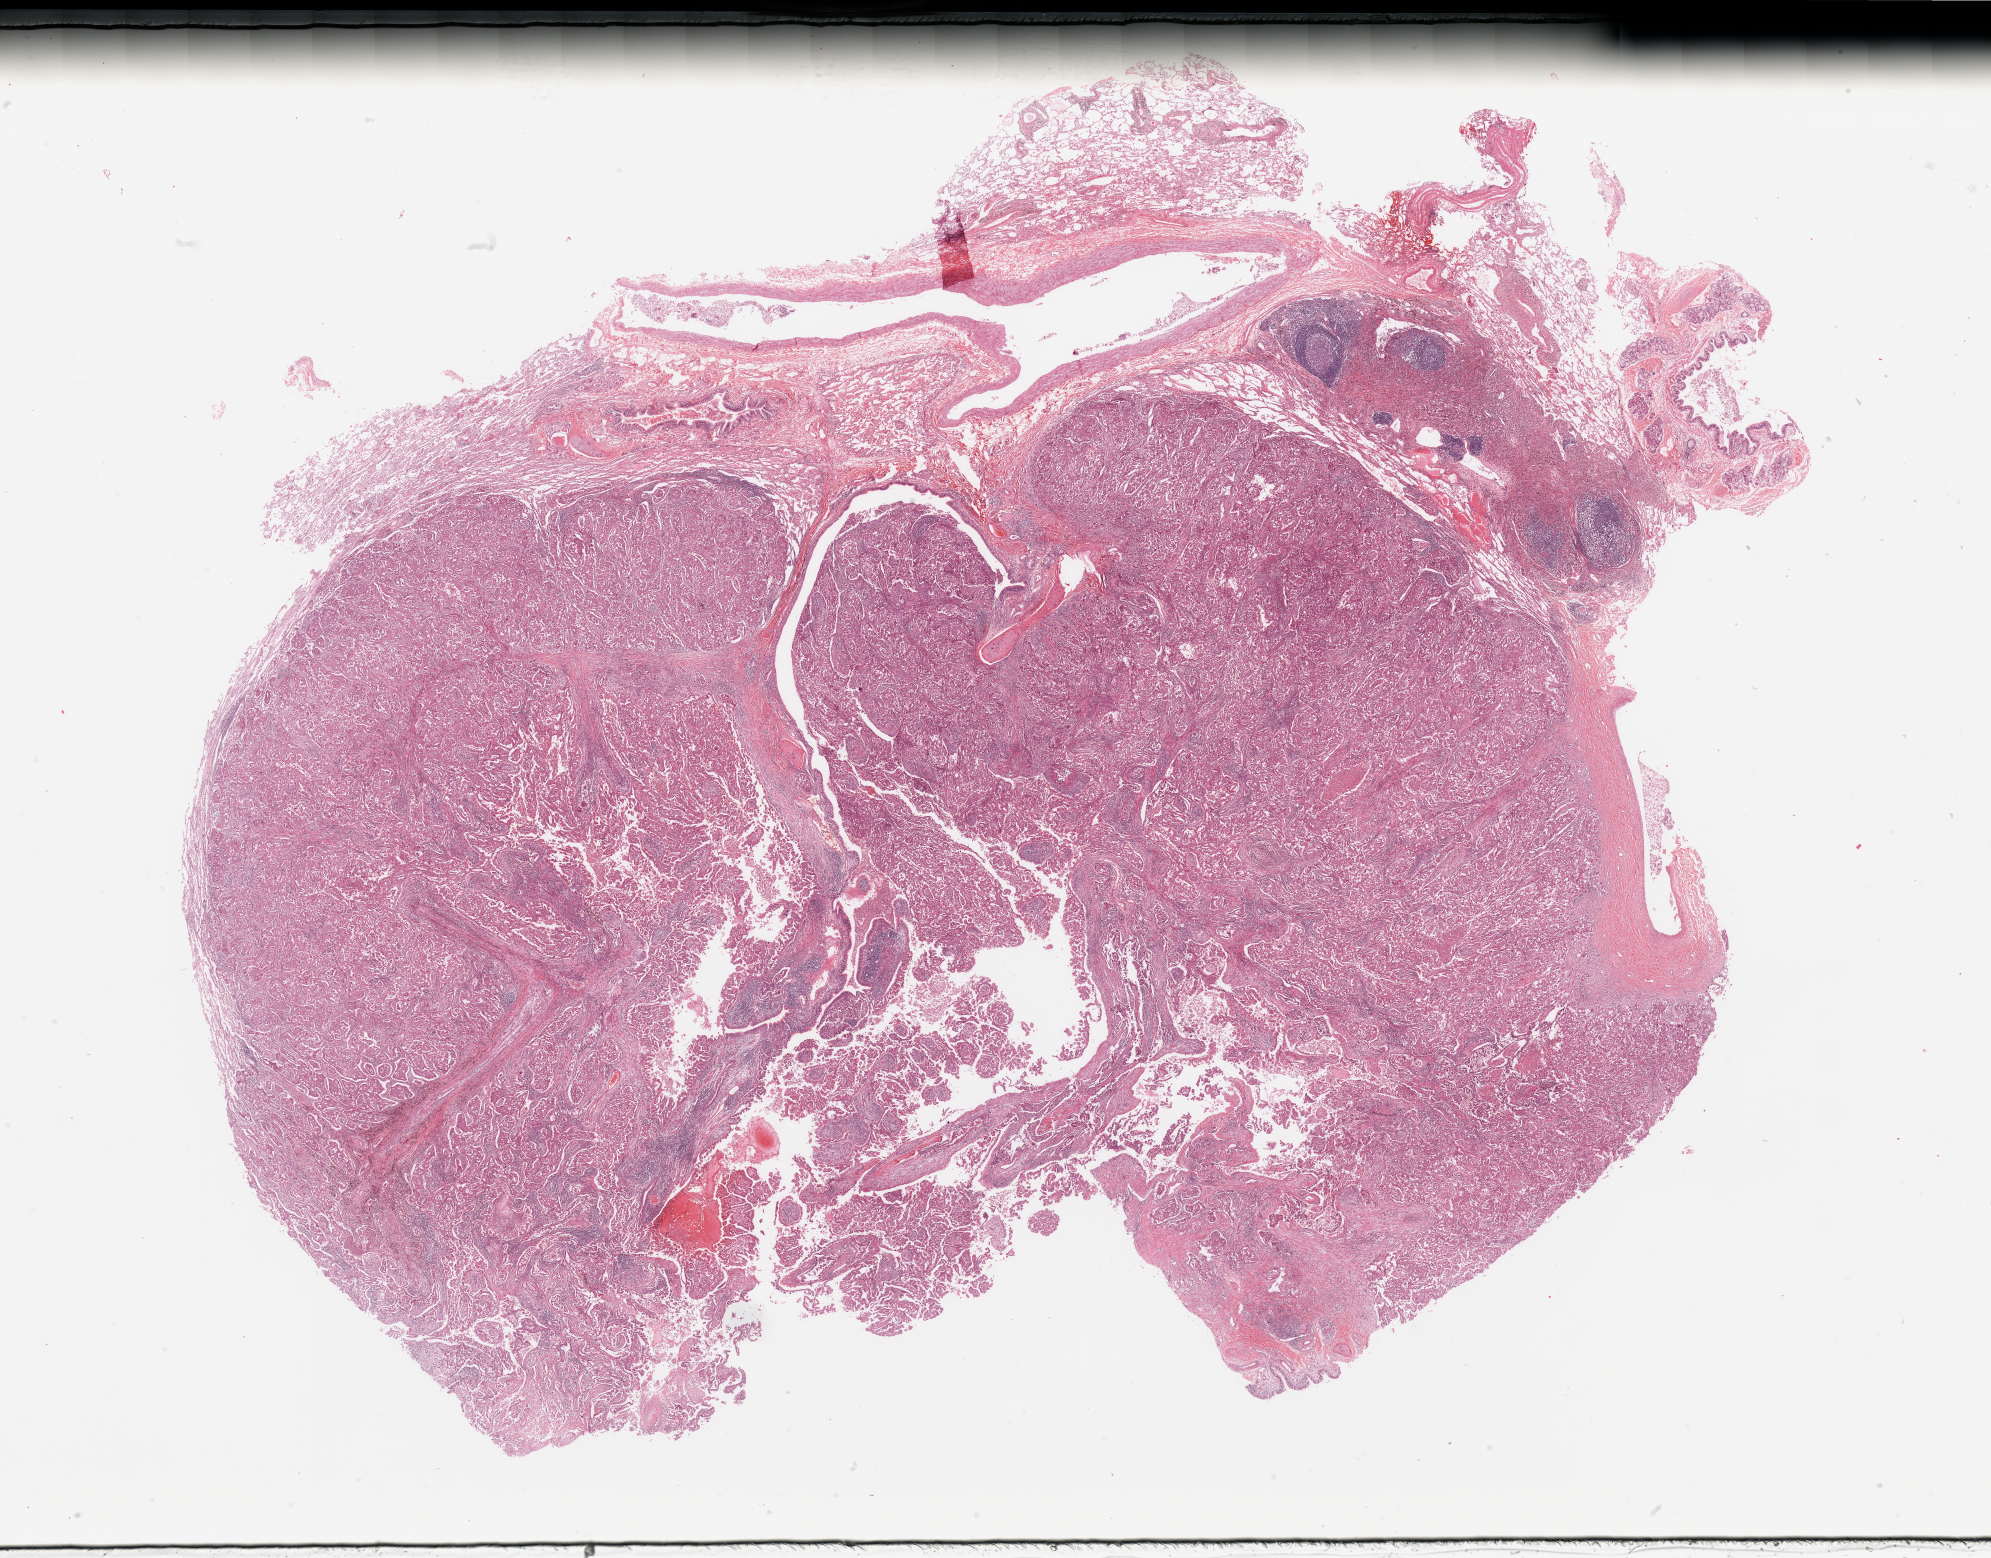
Hematoxylin and eosin (H&E) stained whole-slide image, shown as a low-resolution overview of the whole scanned area (about 31.5 x 24.7 mm, from a 20x scan). Tumour tissue sample, sampled site: lung. Female, 61 y/o. Histologic grade: G3 (poorly differentiated). Pathologist review of this section (percent, as recorded): tumour nuclei 75%, necrosis 2%.
AJCC pathologic stage: IIIA. Histologic diagnosis: Adenocarcinoma, NOS.